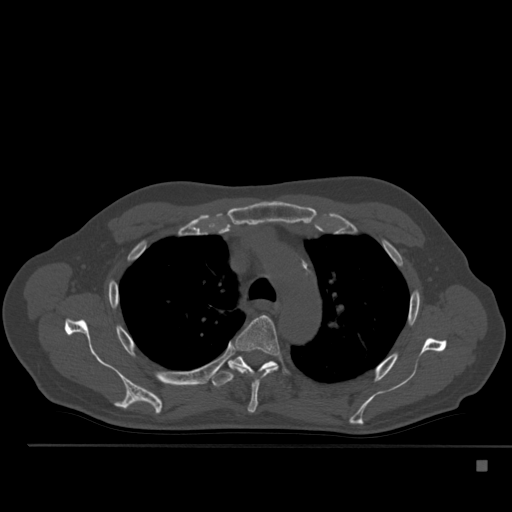
CT including the spine, one axial slice. Slice 376 of 517 in the series (ordered by position). Reconstruction kernel Br40s. 120 kVp. Bone window (W 1800 / L 400 HU). 1.5 mm slice thickness. 512 × 512 image matrix. Male patient, age 70 years. From the clinical record (not read from this slice): primary cancer: renal; vertebrae with lytic lesions (as recorded): T4, T6, T10, T12, L3, L4, L5.
Outlined on this slice (semi-automatically segmented with operator editing):
- T4 vertebra: bounding box <232,315,288,413> (left, top, right, bottom; pixels)
- T5 vertebra: <210,355,284,388>